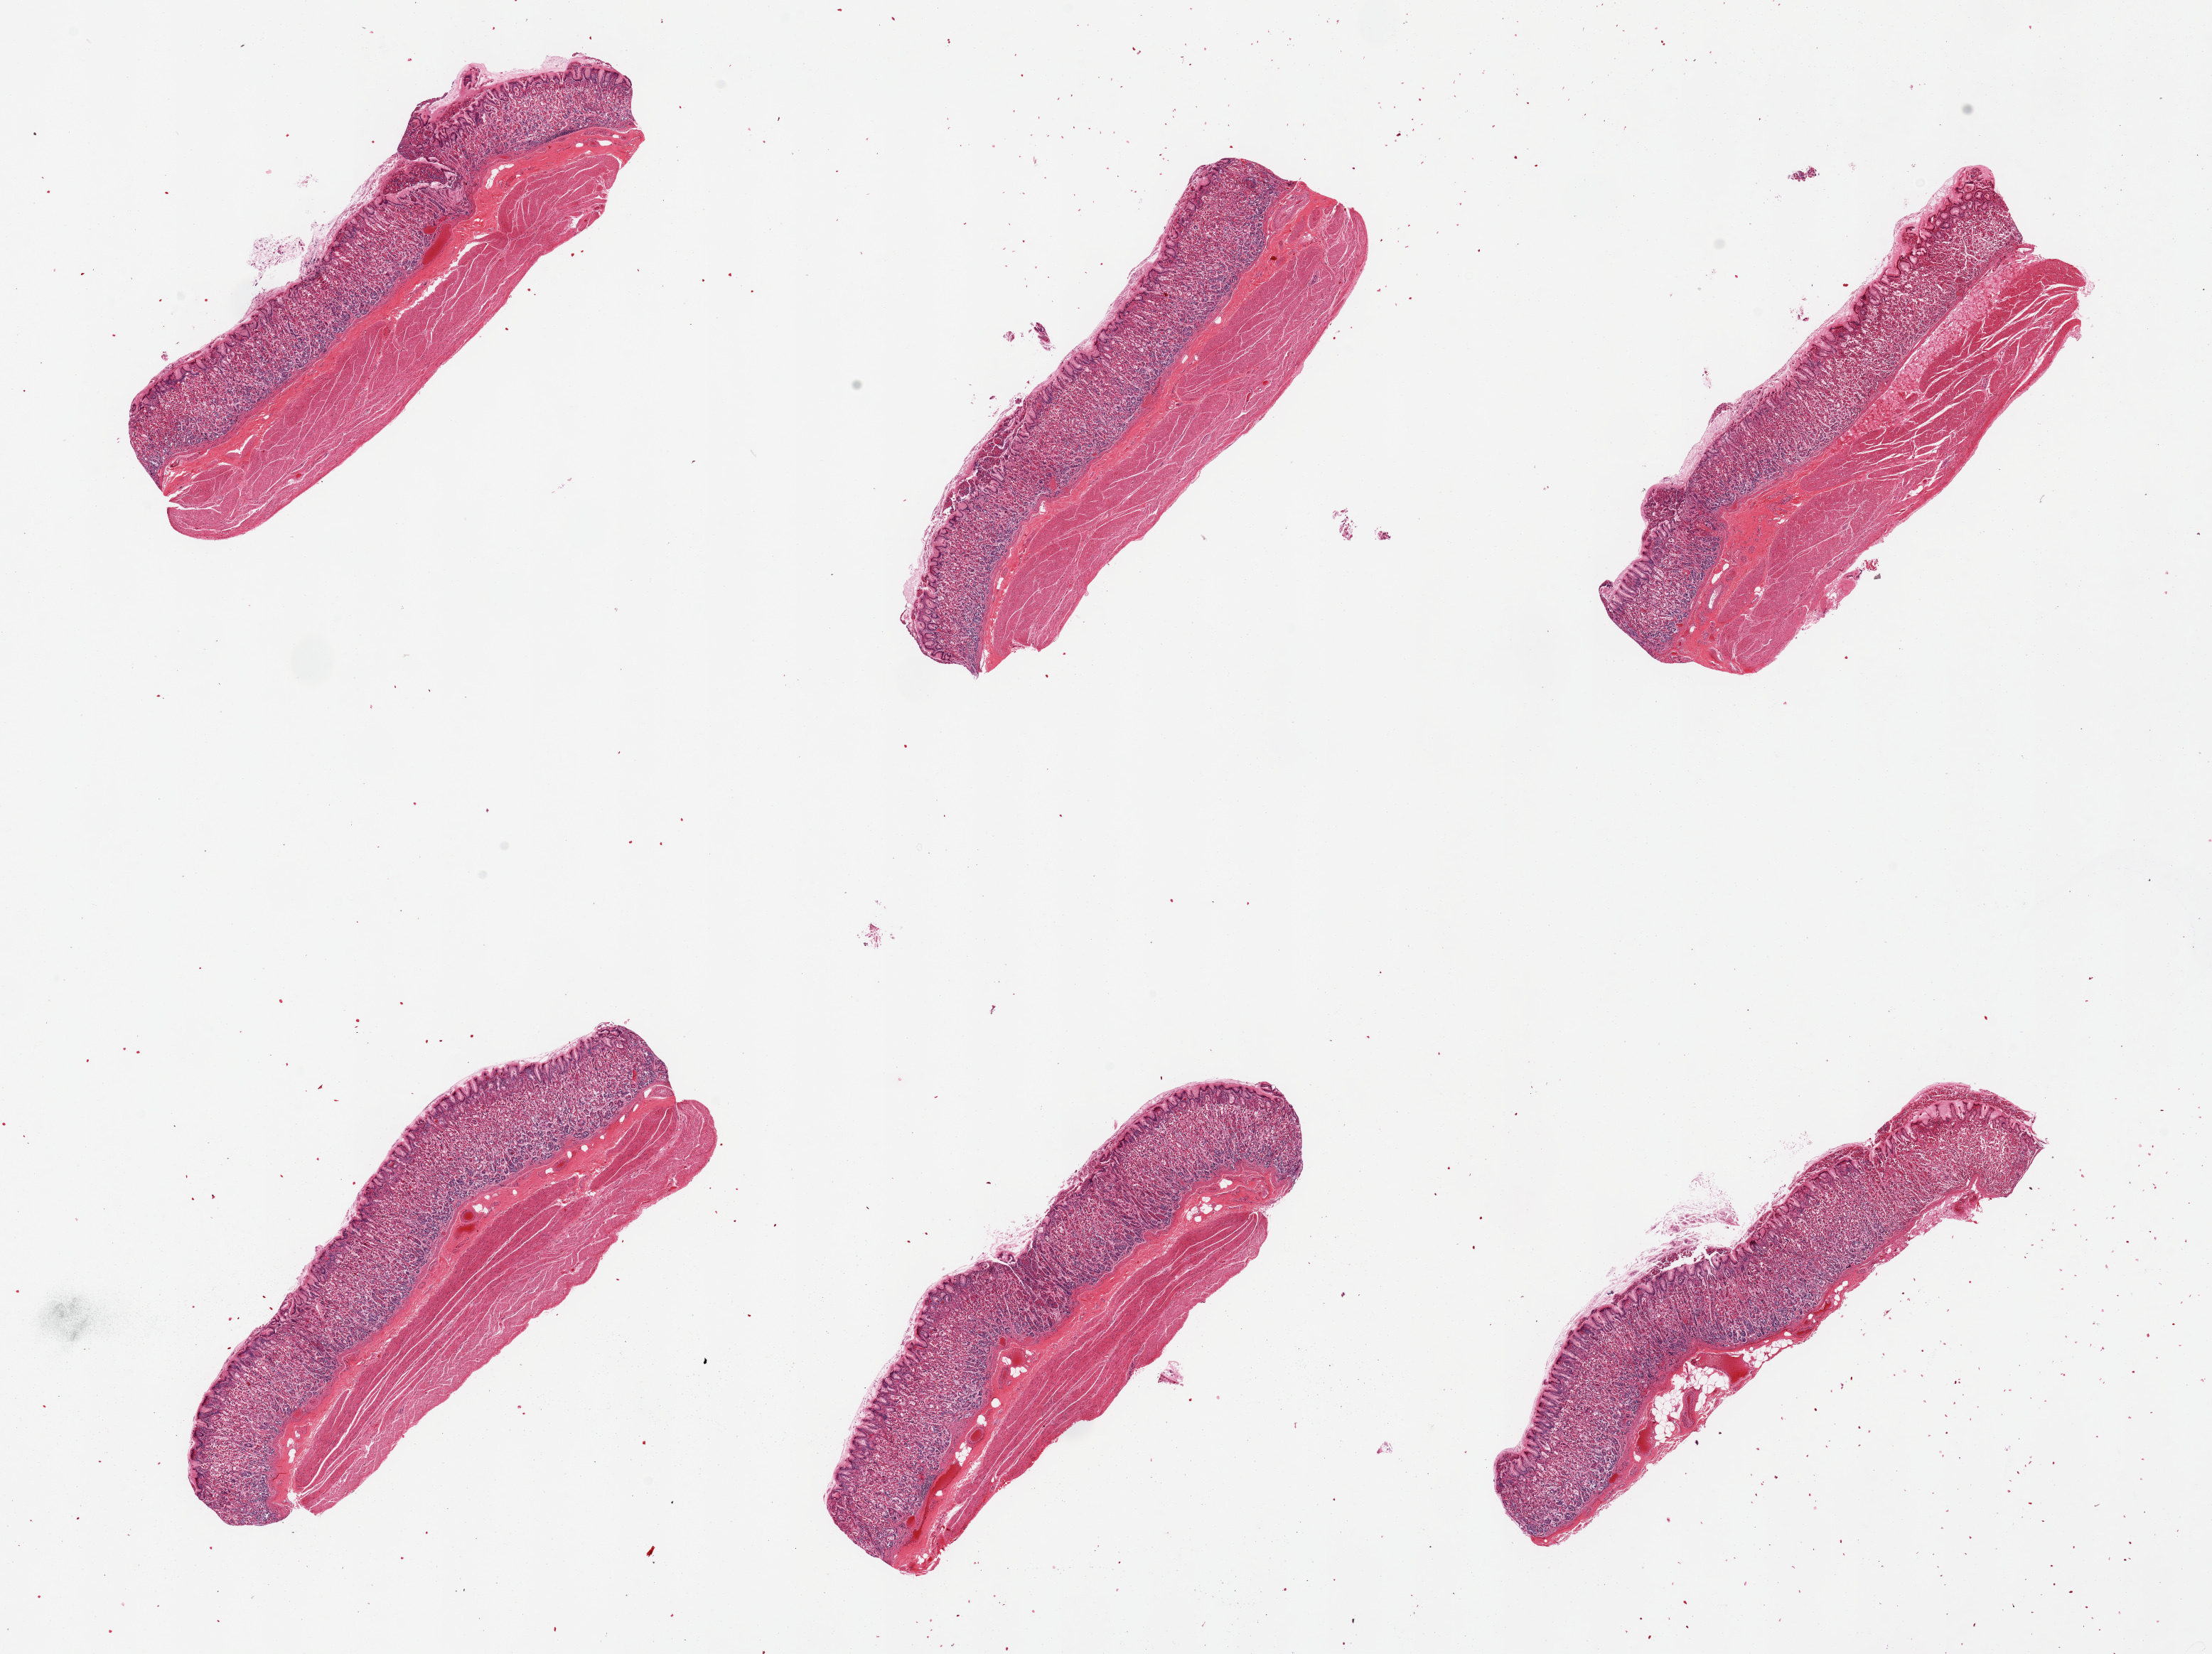
Haematoxylin and eosin whole-slide image, whole scanned area (about 24.6 x 18.4 mm, from a 20x scan) shown as a low-resolution overview, PAXgene-fixed paraffin-embedded (PFPE) section, sampled site (target tissue): stomach, tissue donor sample.
Reviewer comment on this tissue sample: 6 pieces; mucosa is ~1mm, ~40-60% total thickness and fairly well preserved.